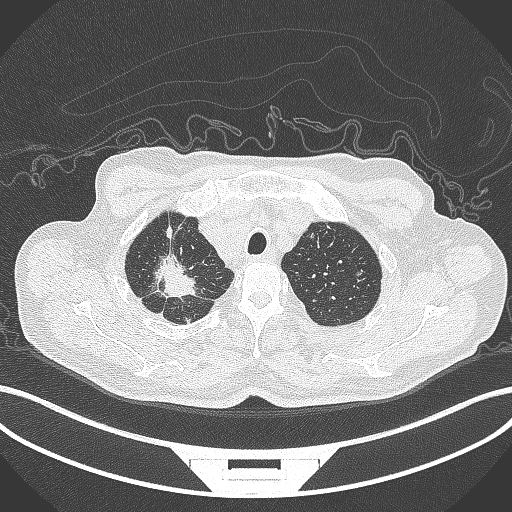
Chest CT, one axial slice. Slice 335 of 407 in the series (ordered by position). 120 kVp. Lung window (W 1500 / L -600 HU). 1 mm slice thickness. 512 × 512 image matrix, field of view 400 × 400 mm. Male patient, age 69 years. Case-level facts recorded for this patient, not image findings: clinical TNM (as recorded): T1c N1 M1.
Outlined on this slice (bounding box drawn by a radiologist):
- lung tumour (recorded histology: adenocarcinoma): bounding box (x1, y1, x2, y2) in pixels: (144, 252, 203, 300)